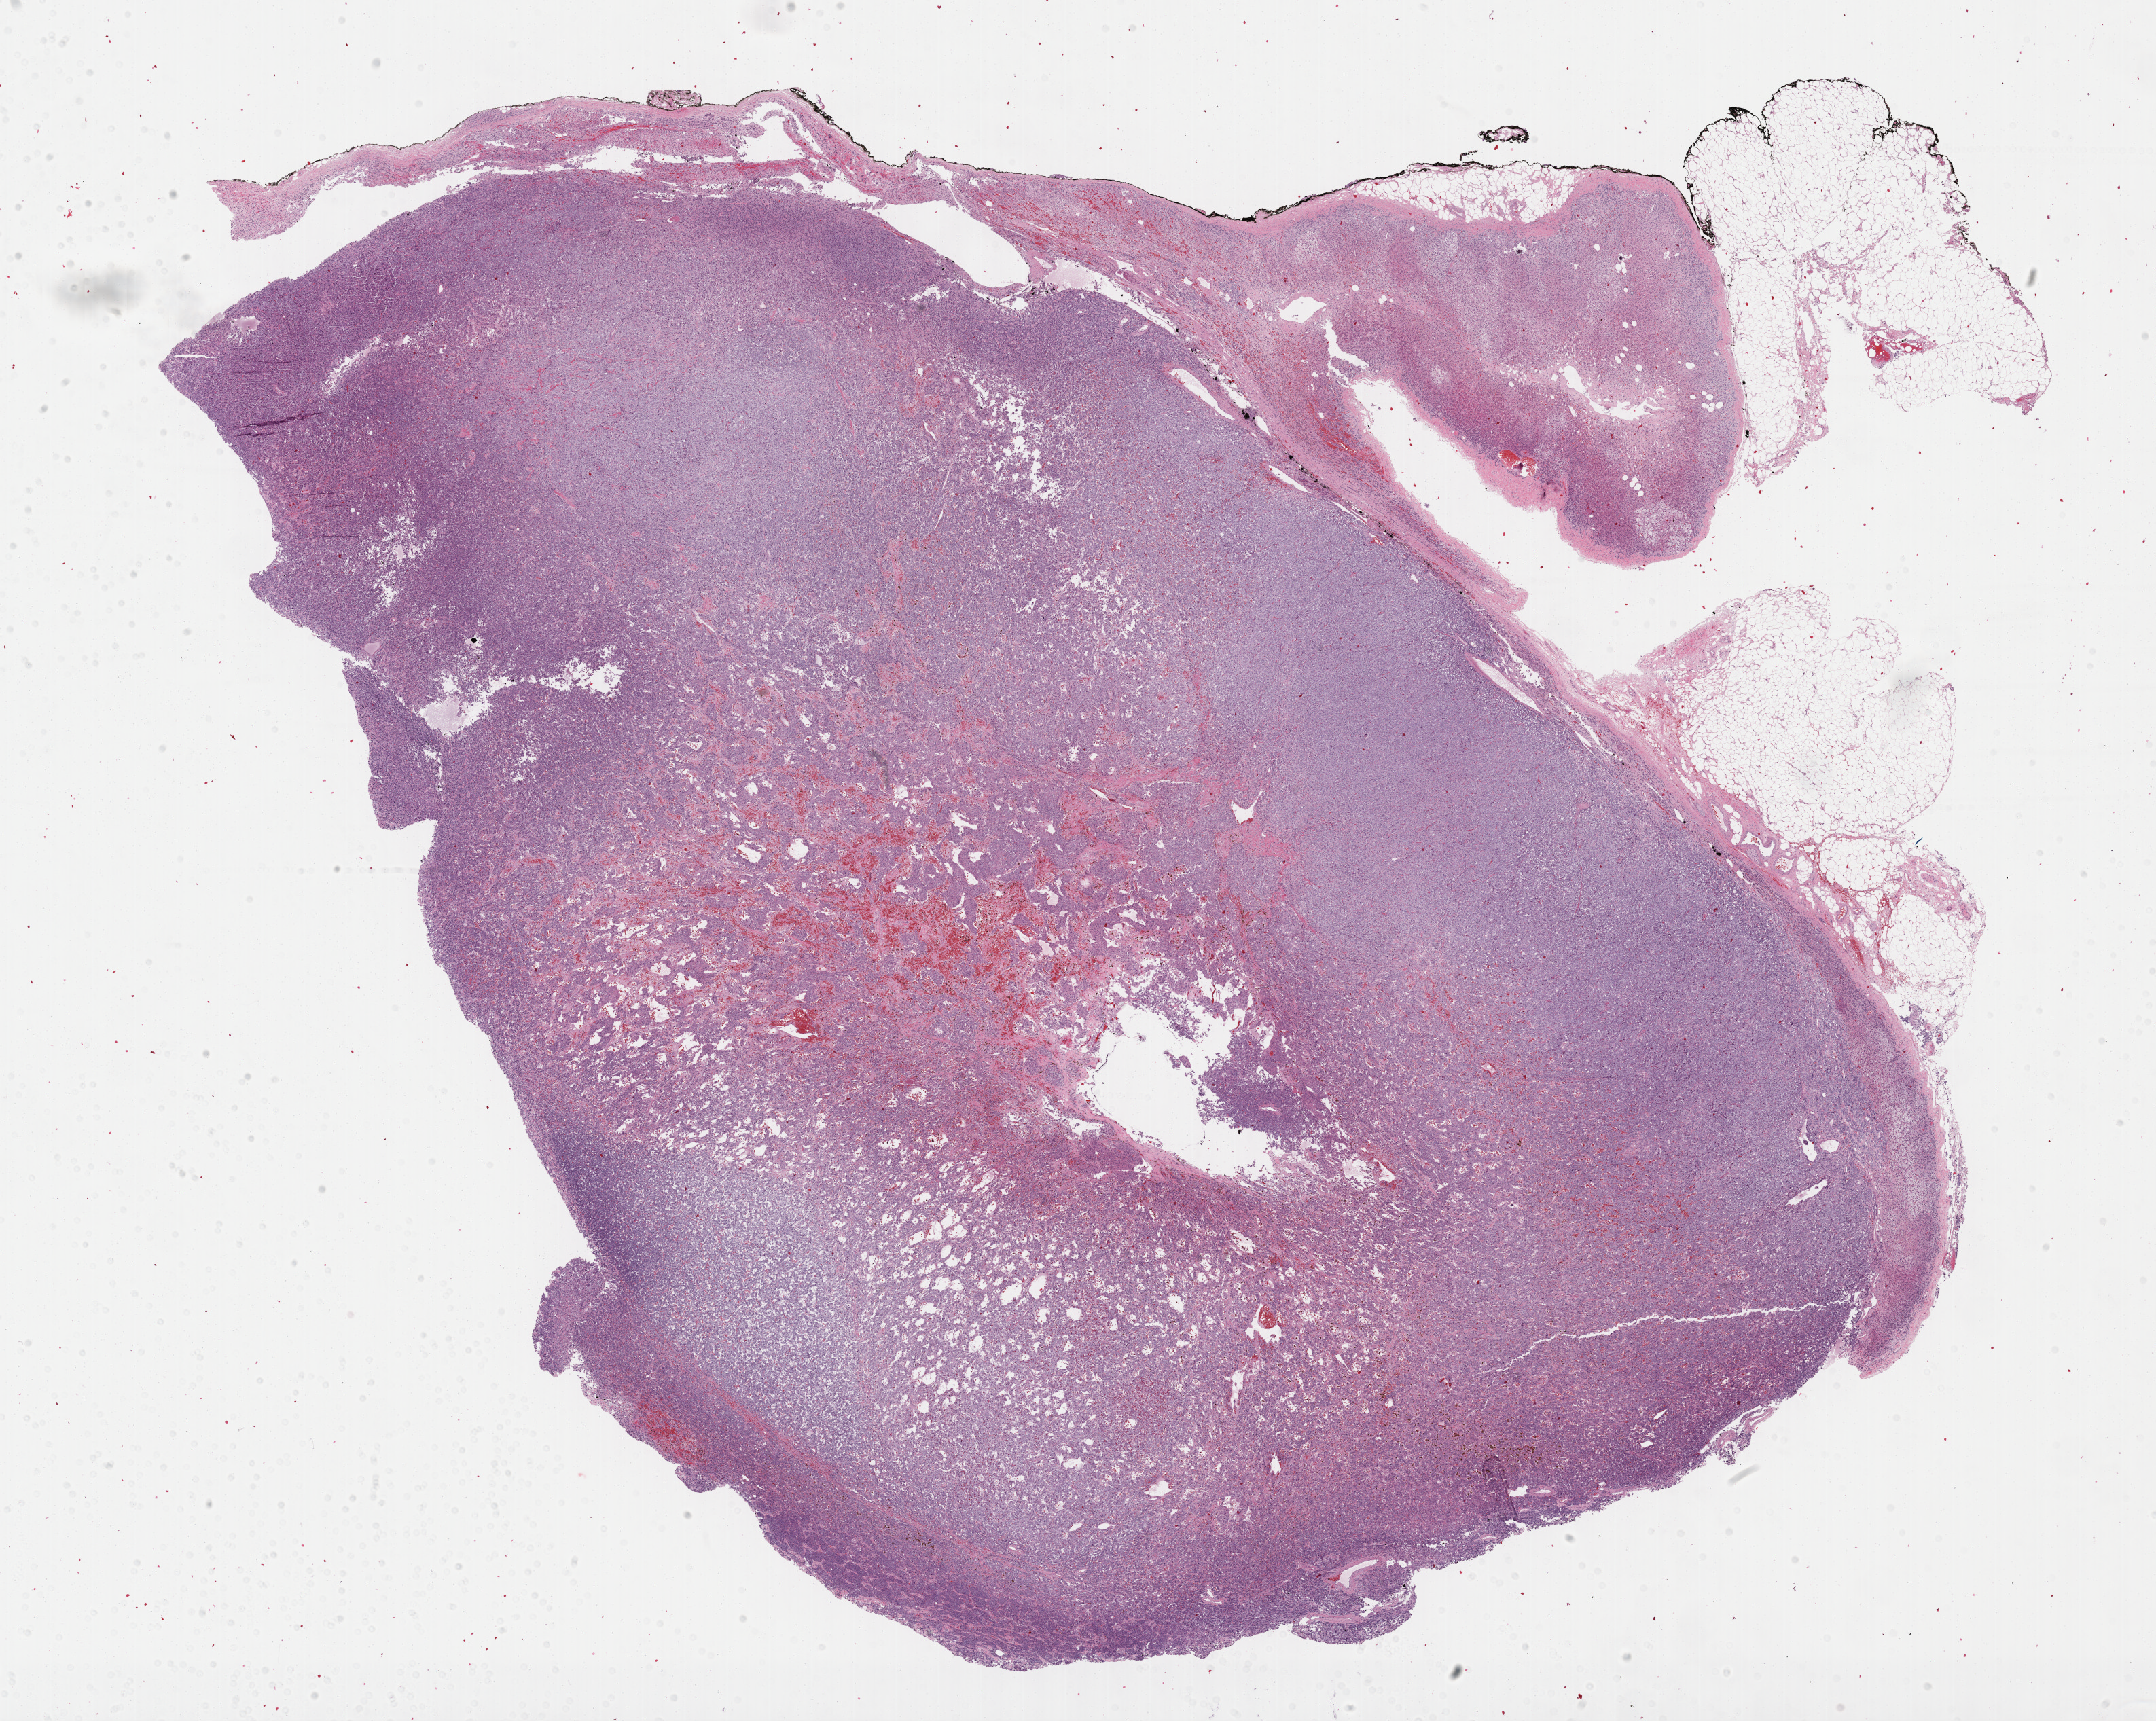
Digitized H&E tissue section (whole slide) — low-resolution overview of the scanned area, about 25.7 x 20.5 mm, formalin-fixed paraffin-embedded (FFPE) diagnostic section, primary tumour sample from the adrenal gland. Female patient; age at initial diagnosis 76 years.
* histologic diagnosis: Pheochromocytoma, NOS